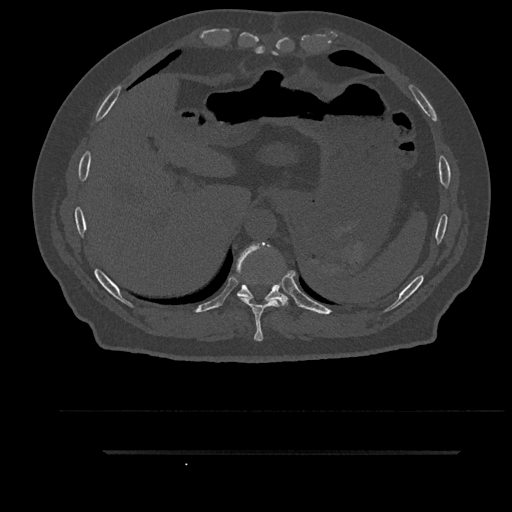
CT including the spine, one axial slice. Slice 395 of 797 in the series (ordered by position). Reconstruction kernel Br40s/3. 120 kVp. Bone window (W 1800 / L 400 HU). 0.5 mm slice thickness. 512 × 512 image matrix, field of view 432 × 432 mm. Patient: male, 63 years. Case-level facts recorded for this patient, not image findings: primary cancer: renal; vertebrae with lytic lesions (as recorded): T8.
Outlined on this slice (semi-automatic segmentation, software-assisted and operator-edited):
- T10 vertebra: bounding box <236,242,288,307> (left, top, right, bottom; pixels)
- T9 vertebra: <236,242,288,341>